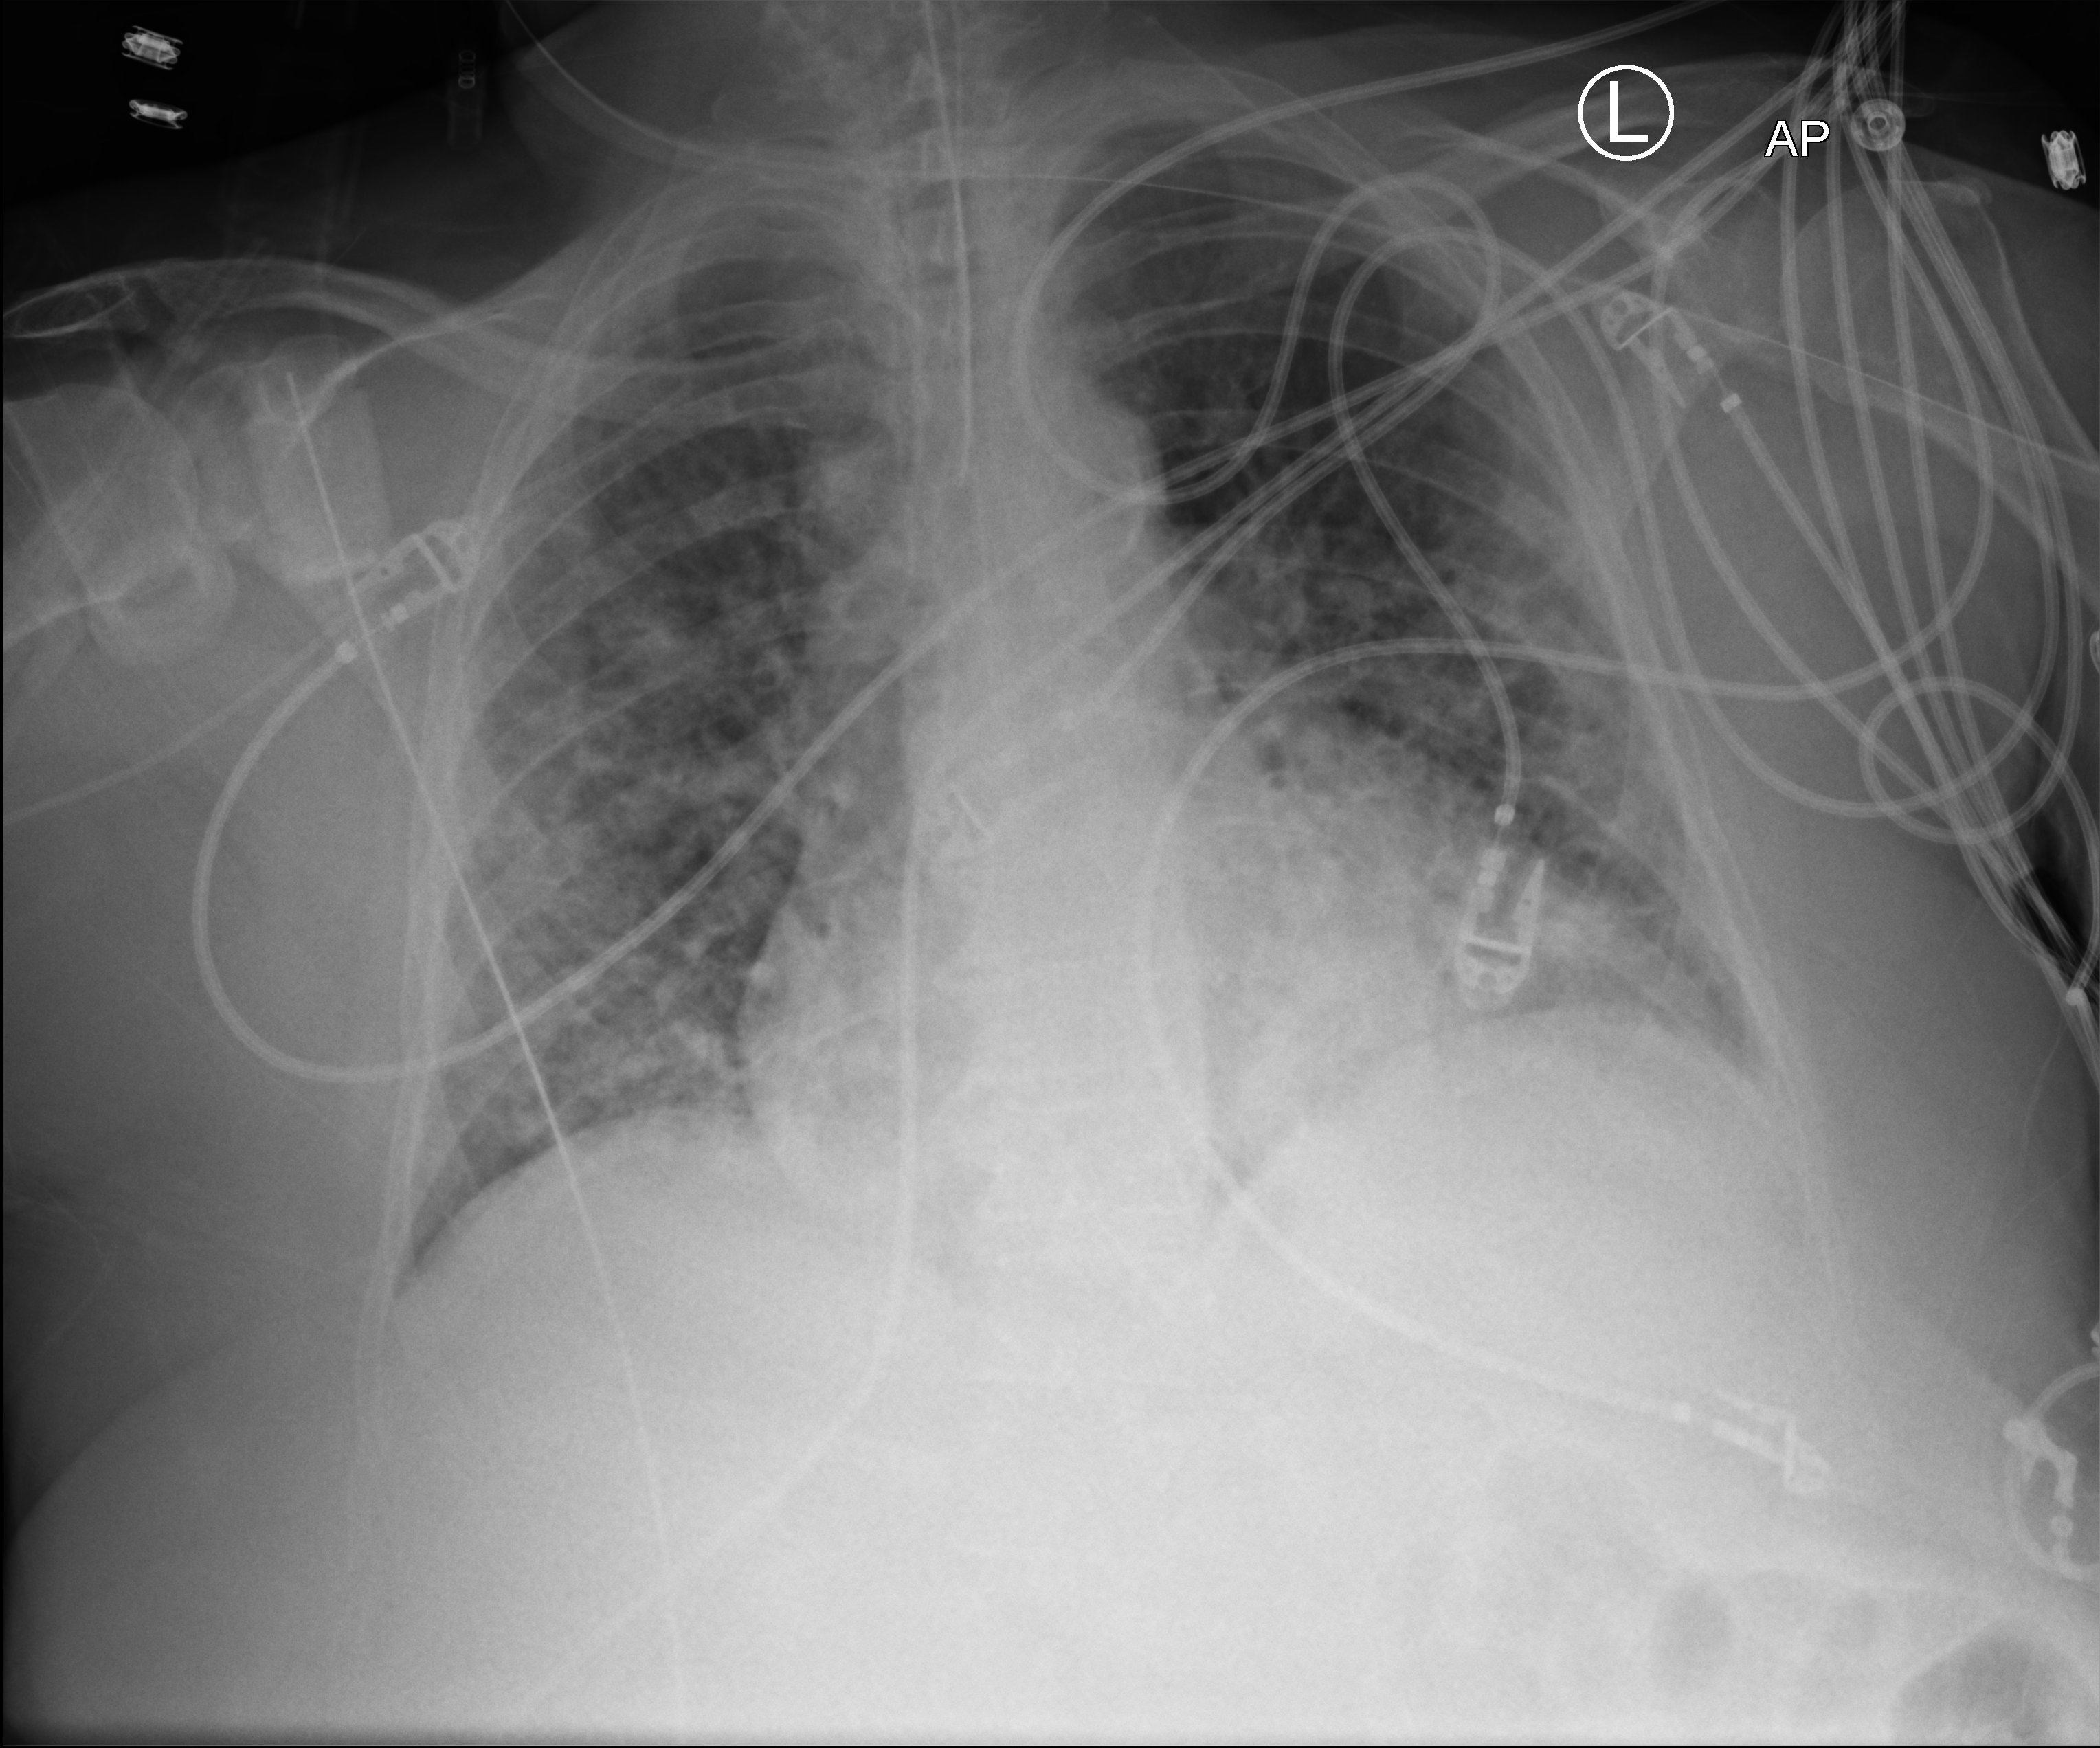
Portable chest radiograph; anteroposterior (AP) projection. Female patient hospitalised with COVID-19, age 75–90 years.
Hospital-stay facts (about this admission, not read from this image; timing relative to this image not recorded):
- mechanically ventilated during this hospital stay: yes
- length of hospital stay: 31 days